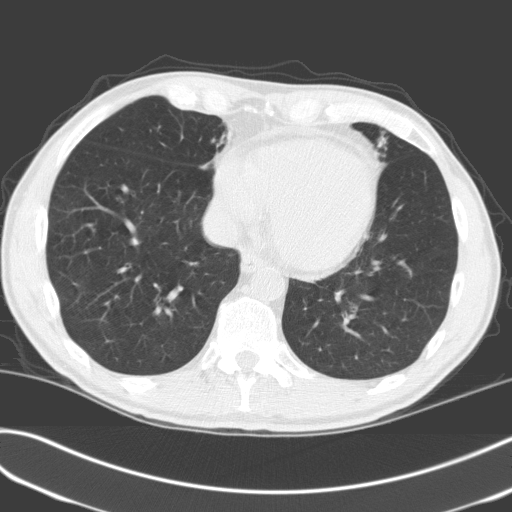
Low-dose screening chest CT, one axial slice; position 56 of 170 along the scan axis; 120 kVp; lung window (W 1500 / L -600 HU); 3.2 mm slice thickness; 512 × 512 image matrix.
Outlined on this slice (expert manual segmentation):
- lesion 1 (tumor, upper lobe of left lung): bounding box [x1, y1, x2, y2] px = [378, 137, 386, 147]